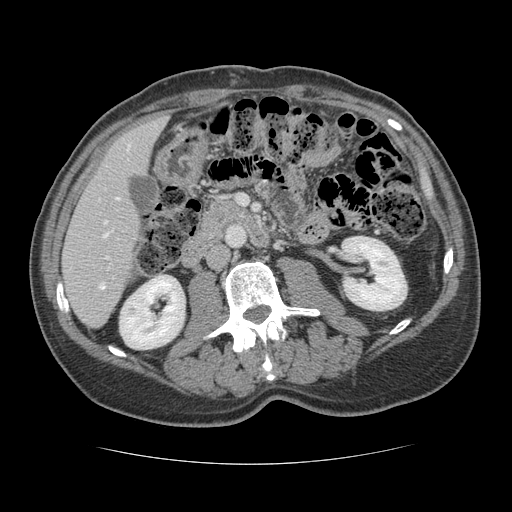
Contrast-enhanced abdominal CT, one axial slice; position 50 of 134 along the scan axis; 120 kVp; intravenous contrast given; soft-tissue window (W 400 / L 40 HU); 2.5 mm slice thickness; 512 × 512 image matrix. Male patient, age 68 years. Case-level facts recorded for this patient, not image findings: diagnosis: colorectal cancer liver metastases, imaged before liver resection; multiple liver metastases: yes; largest metastasis: 2.2 cm; disease in both lobes: no.
Structures marked on this image (expert manual segmentation):
- hepatic veins: box from (x=104, y=149) to (x=129, y=237) px
- liver: (x=64, y=116)–(x=166, y=327)
- planned liver remnant (the part of the liver to remain after resection): (x=64, y=117)–(x=165, y=327)
- portal vein (with intrahepatic branches): (x=100, y=256)–(x=109, y=289)